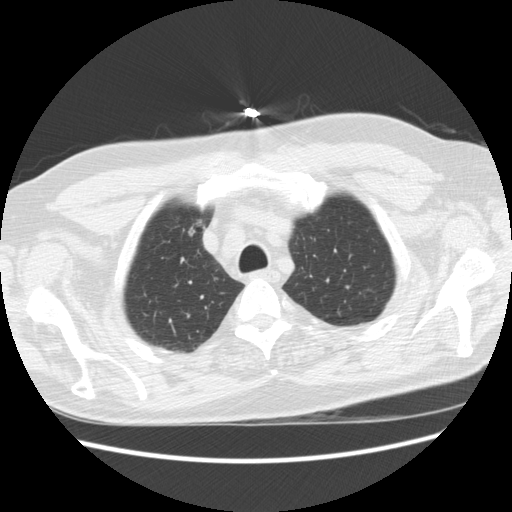
Axial slice from a low-dose chest CT screening exam. Baseline annual screen. Lung window (W 1500 / L -600 HU). Standard (soft-tissue) reconstruction kernel (STANDARD). Slice 44 of 241 in the series. 512 × 512 image matrix. Male participant, aged 66 years at enrolment.
Expert-annotated lung lesion, bounding box [x1, y1, x2, y2] px = [171, 211, 211, 247]. No non-calcified nodule or mass ≥4 mm was recorded by the screening reader at this exam. Participant outcome: lung cancer diagnosed 951 days after this screen — bronchiolo-alveolar adenocarcinoma, NOS, right upper lobe, moderately differentiated (G2), stage IA (AJCC 6th edition), 12 mm at pathology.